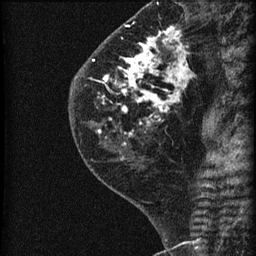
Breast MRI (dynamic contrast-enhanced), one sagittal slice. Slice 24 of 60 in the series (ordered by position). Dynamic contrast-enhanced series, image 2 of 3 at this slice position (ordered by acquisition). 1.5 T. TE 4.2 ms, TR 22.7 ms. 1.8 mm slice thickness. 256 × 256 image matrix, field of view 180 × 180 mm. Female patient, age 45 years. Case-level facts recorded for this patient, not image findings: setting: breast cancer imaged before/during neoadjuvant chemotherapy; receptor status: HR-positive, HER2-negative.
Annotated regions visible in this slice (semi-automatic segmentation, software-assisted and operator-edited):
- analysis volume of interest (the breast-tissue region the enhancement analysis was run in; not a lesion): bounding box [x1, y1, x2, y2] px = [74, 11, 205, 140]
- tumour enhancement mask (voxels above the 90 % enhancement threshold inside the analysis volume of interest): [93, 27, 187, 135]